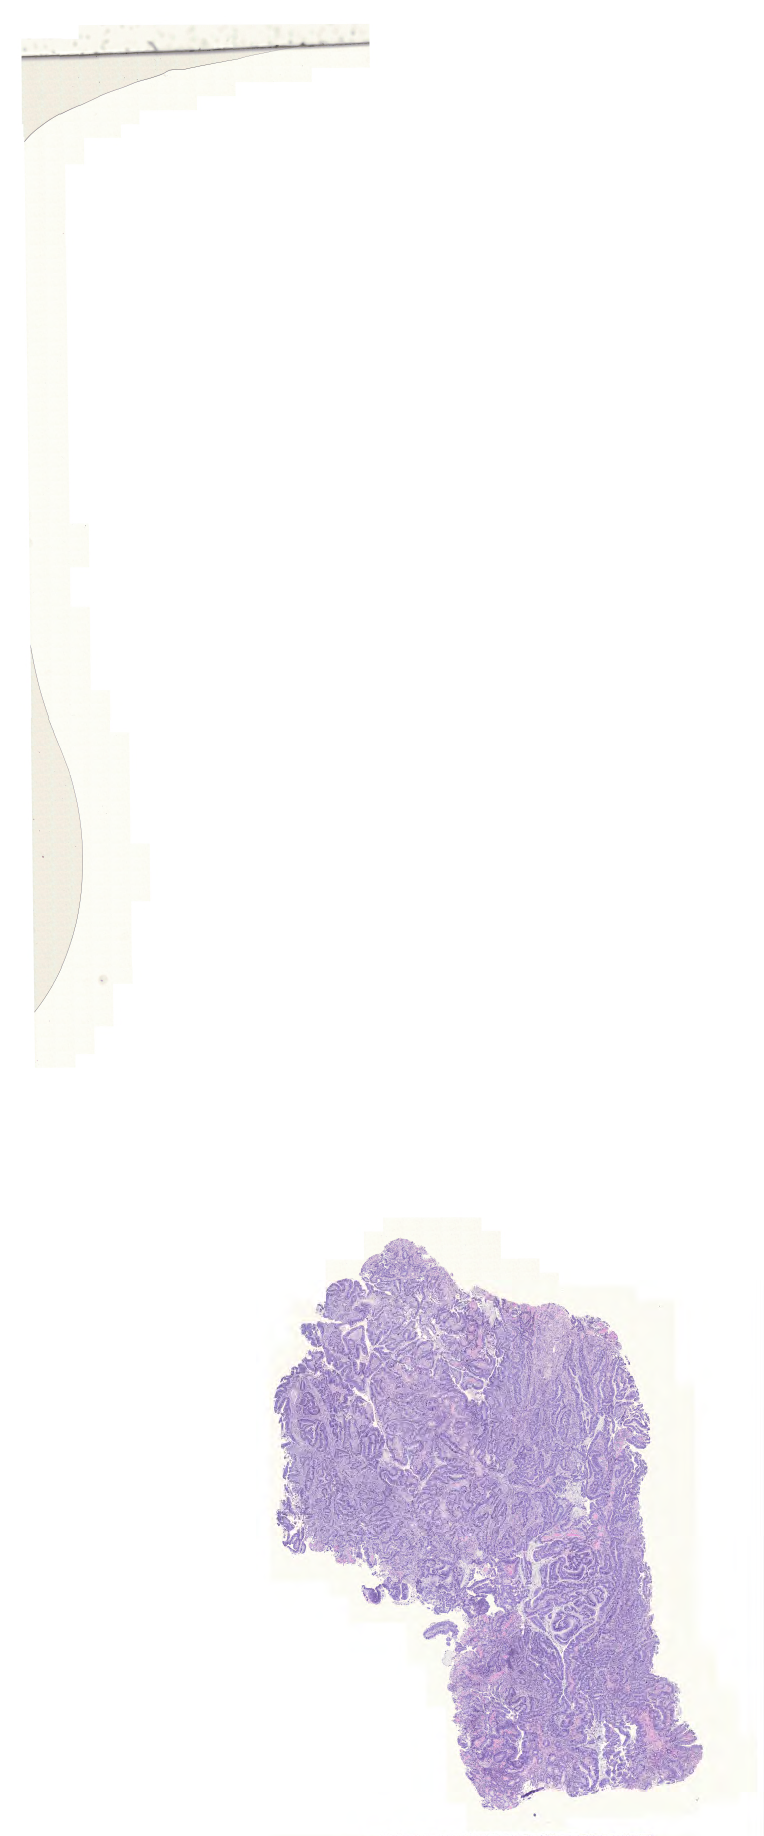
Digitized H&E tissue section (whole slide) — low-resolution overview of the scanned area, about 11.4 x 27.3 mm; formalin-fixed paraffin-embedded (FFPE) diagnostic section; colon, primary tumour sample. Male patient; age at initial diagnosis 74 years.
* AJCC pathologic stage: IIA (6th edition)
* histologic diagnosis: Adenocarcinoma, NOS
* lymph nodes positive (case pathology): 0 of 14 examined